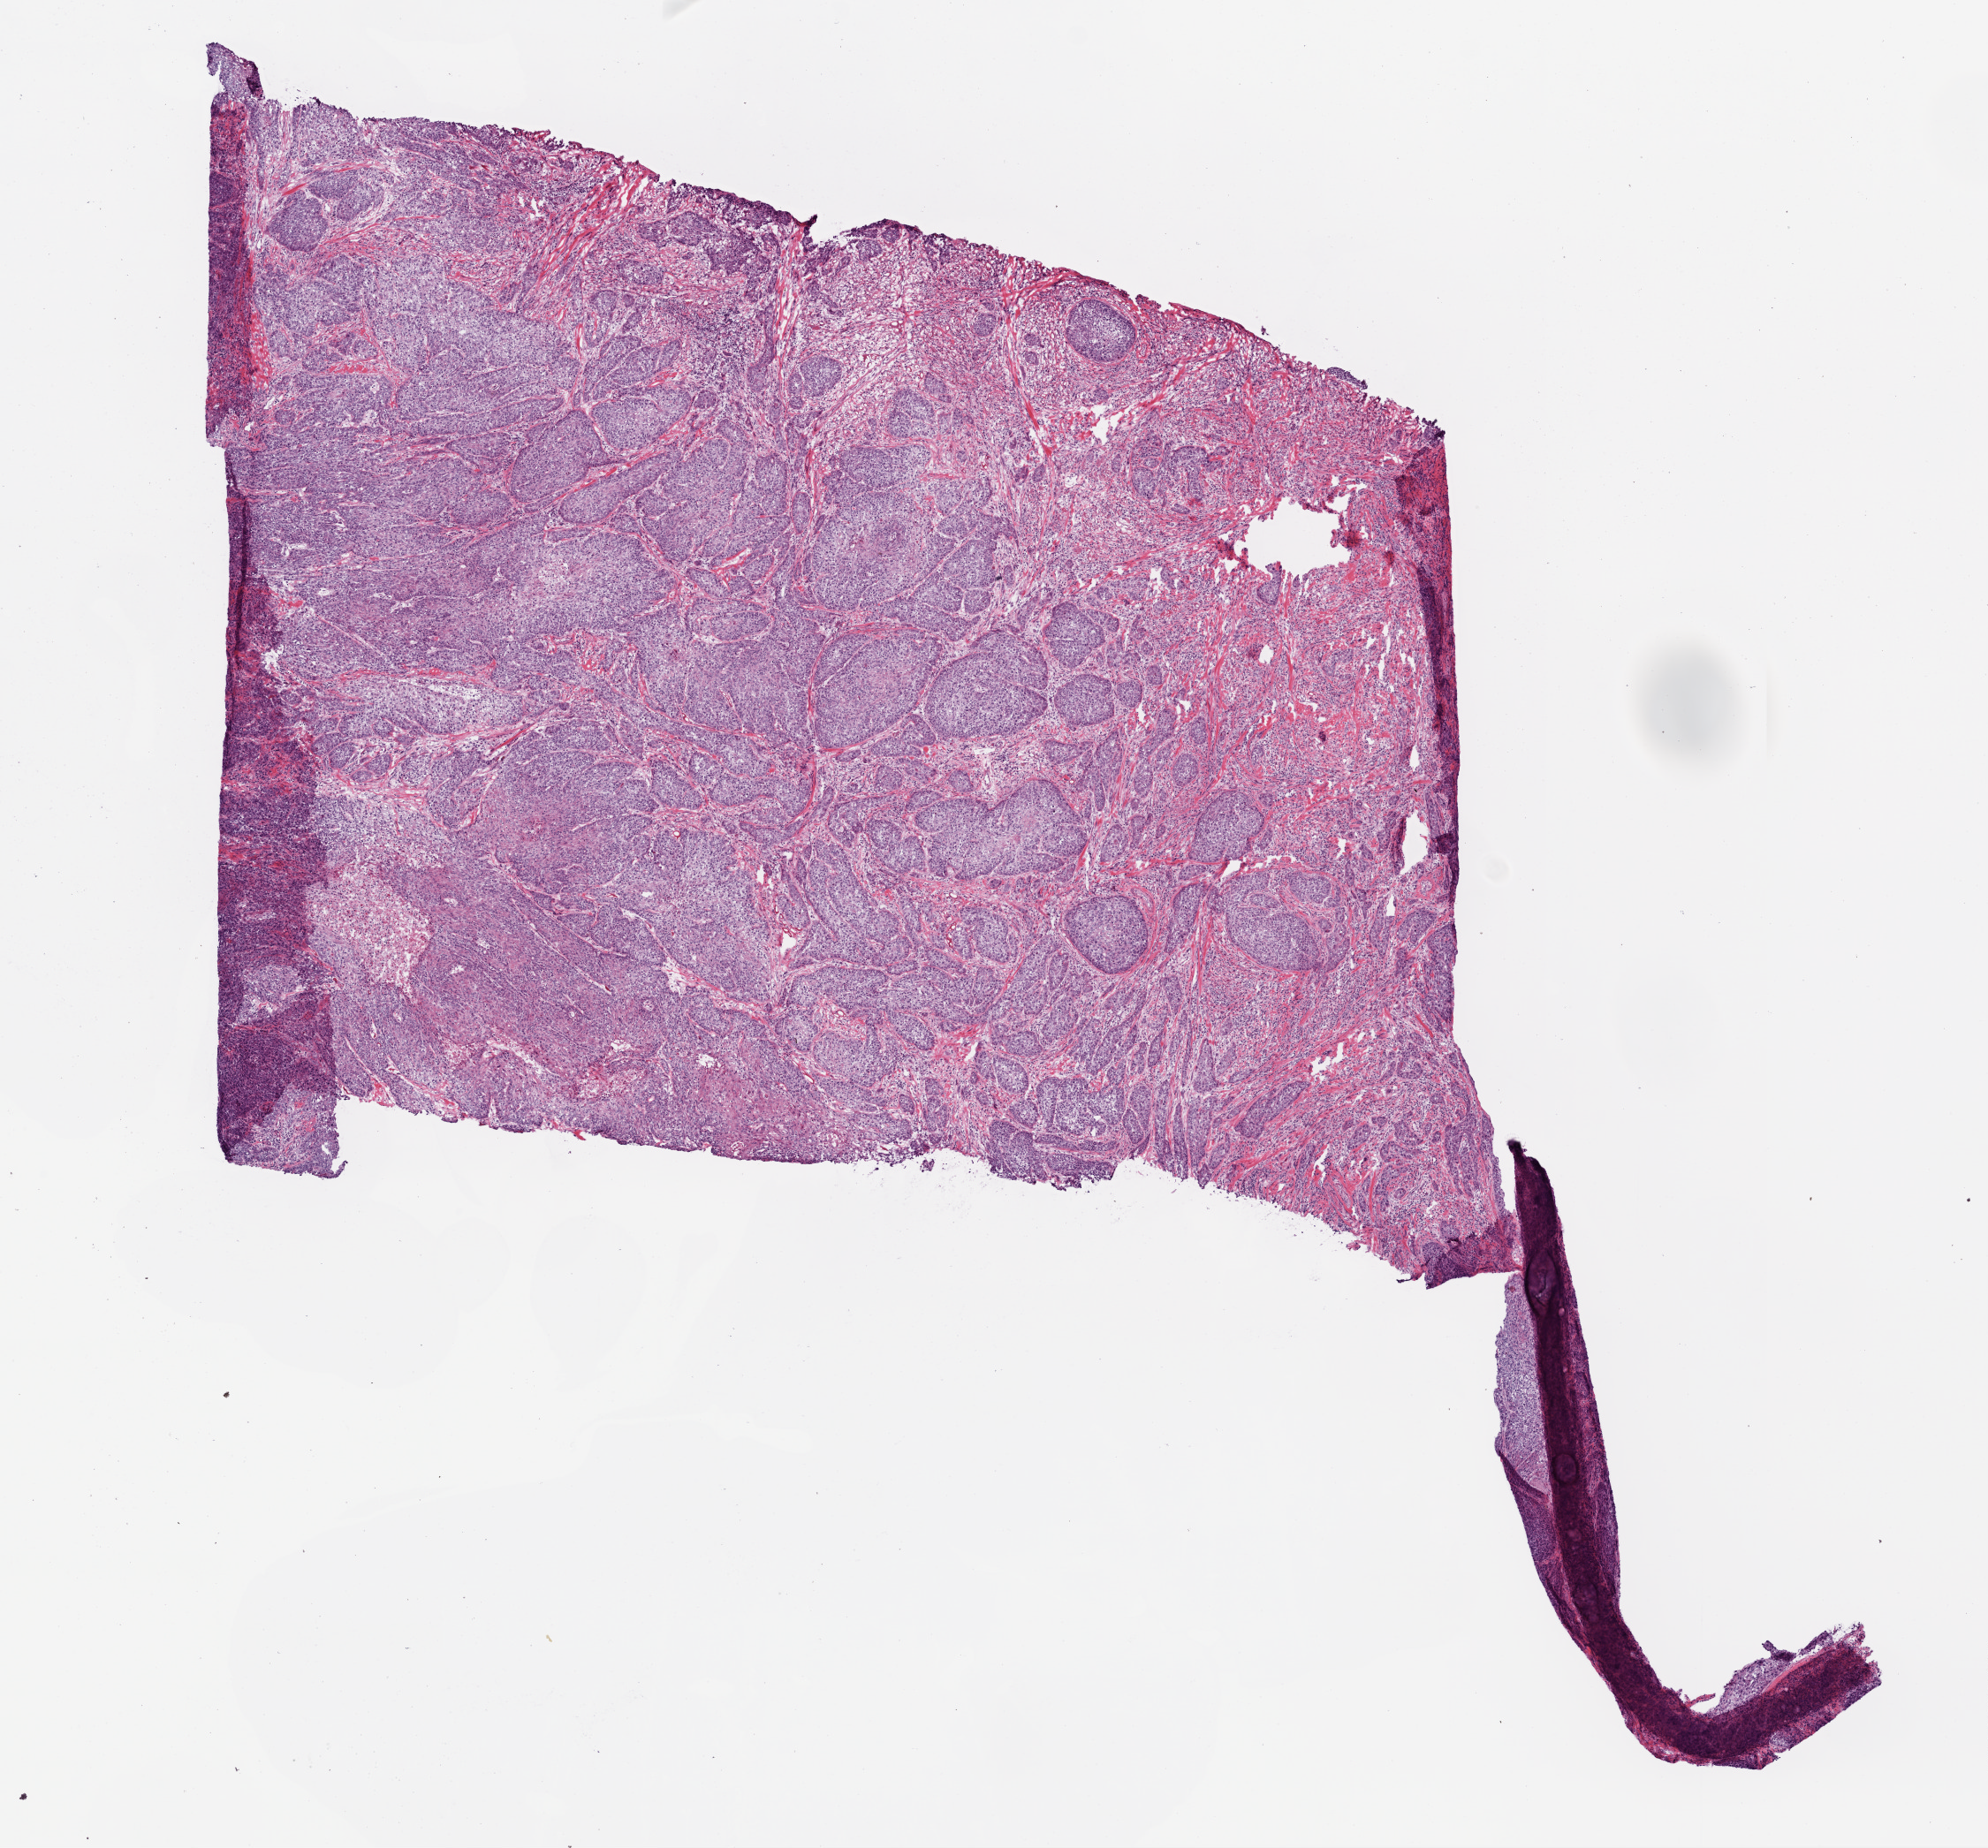
Whole-slide histology image, H&E, whole scanned area (about 9.0 x 8.4 mm) shown as a low-resolution overview. Frozen section from the top of the tissue portion. Head and neck, primary tumour sample. Patient: female, age at initial diagnosis 45 years. Histologic grade: G2 (moderately differentiated). Composition of this section per pathologist review: tumour cells 85%, tumour nuclei 85%, normal cells 0%, stromal cells 10%, necrosis 5%.
Histologic diagnosis: Squamous cell carcinoma, NOS (tongue, NOS). AJCC pathologic stage: IVA (6th edition). Laterality: right.